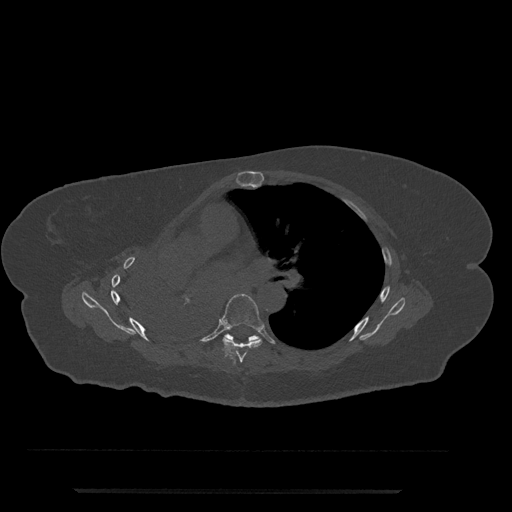
CT including the spine, one axial slice. Slice 481 of 797 in the series (ordered by position). 120 kVp. Bone window (W 1800 / L 400 HU). 0.5 mm slice thickness. 512 × 512 image matrix, field of view 440 × 440 mm. Patient: female, 51 years. From the clinical record (not read from this slice): primary cancer: neuro.
Outlined on this slice (semi-automatic segmentation, software-assisted and operator-edited):
- T6 vertebra: bounding box [x1, y1, x2, y2] px = [220, 294, 264, 364]
- T7 vertebra: [225, 333, 260, 341]